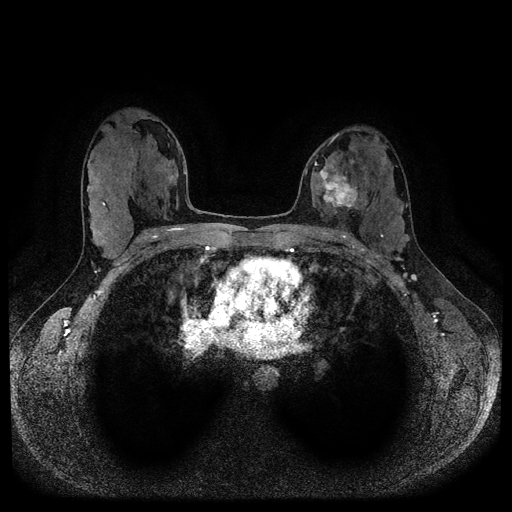
Breast MRI (dynamic contrast-enhanced, multi-phase), one axial slice. Slice 60 of 116 in the series (ordered by position). Dynamic contrast-enhanced series, time point 2 of 5 at this slice position (early post-contrast). 1.5 T. TE 2.6 ms, TR 5.3 ms. 2 mm slice thickness. 512 × 512 image matrix, field of view 350 × 350 mm. Female patient, age 33 years.
Outlined on this slice (semi-automatic segmentation, software-assisted and operator-edited):
- breast lesion (labelled 'tumour' in the annotation; benign lesions carry a separate 'benign' label): bounding box (x1, y1, x2, y2) in pixels: (318, 167, 361, 214)